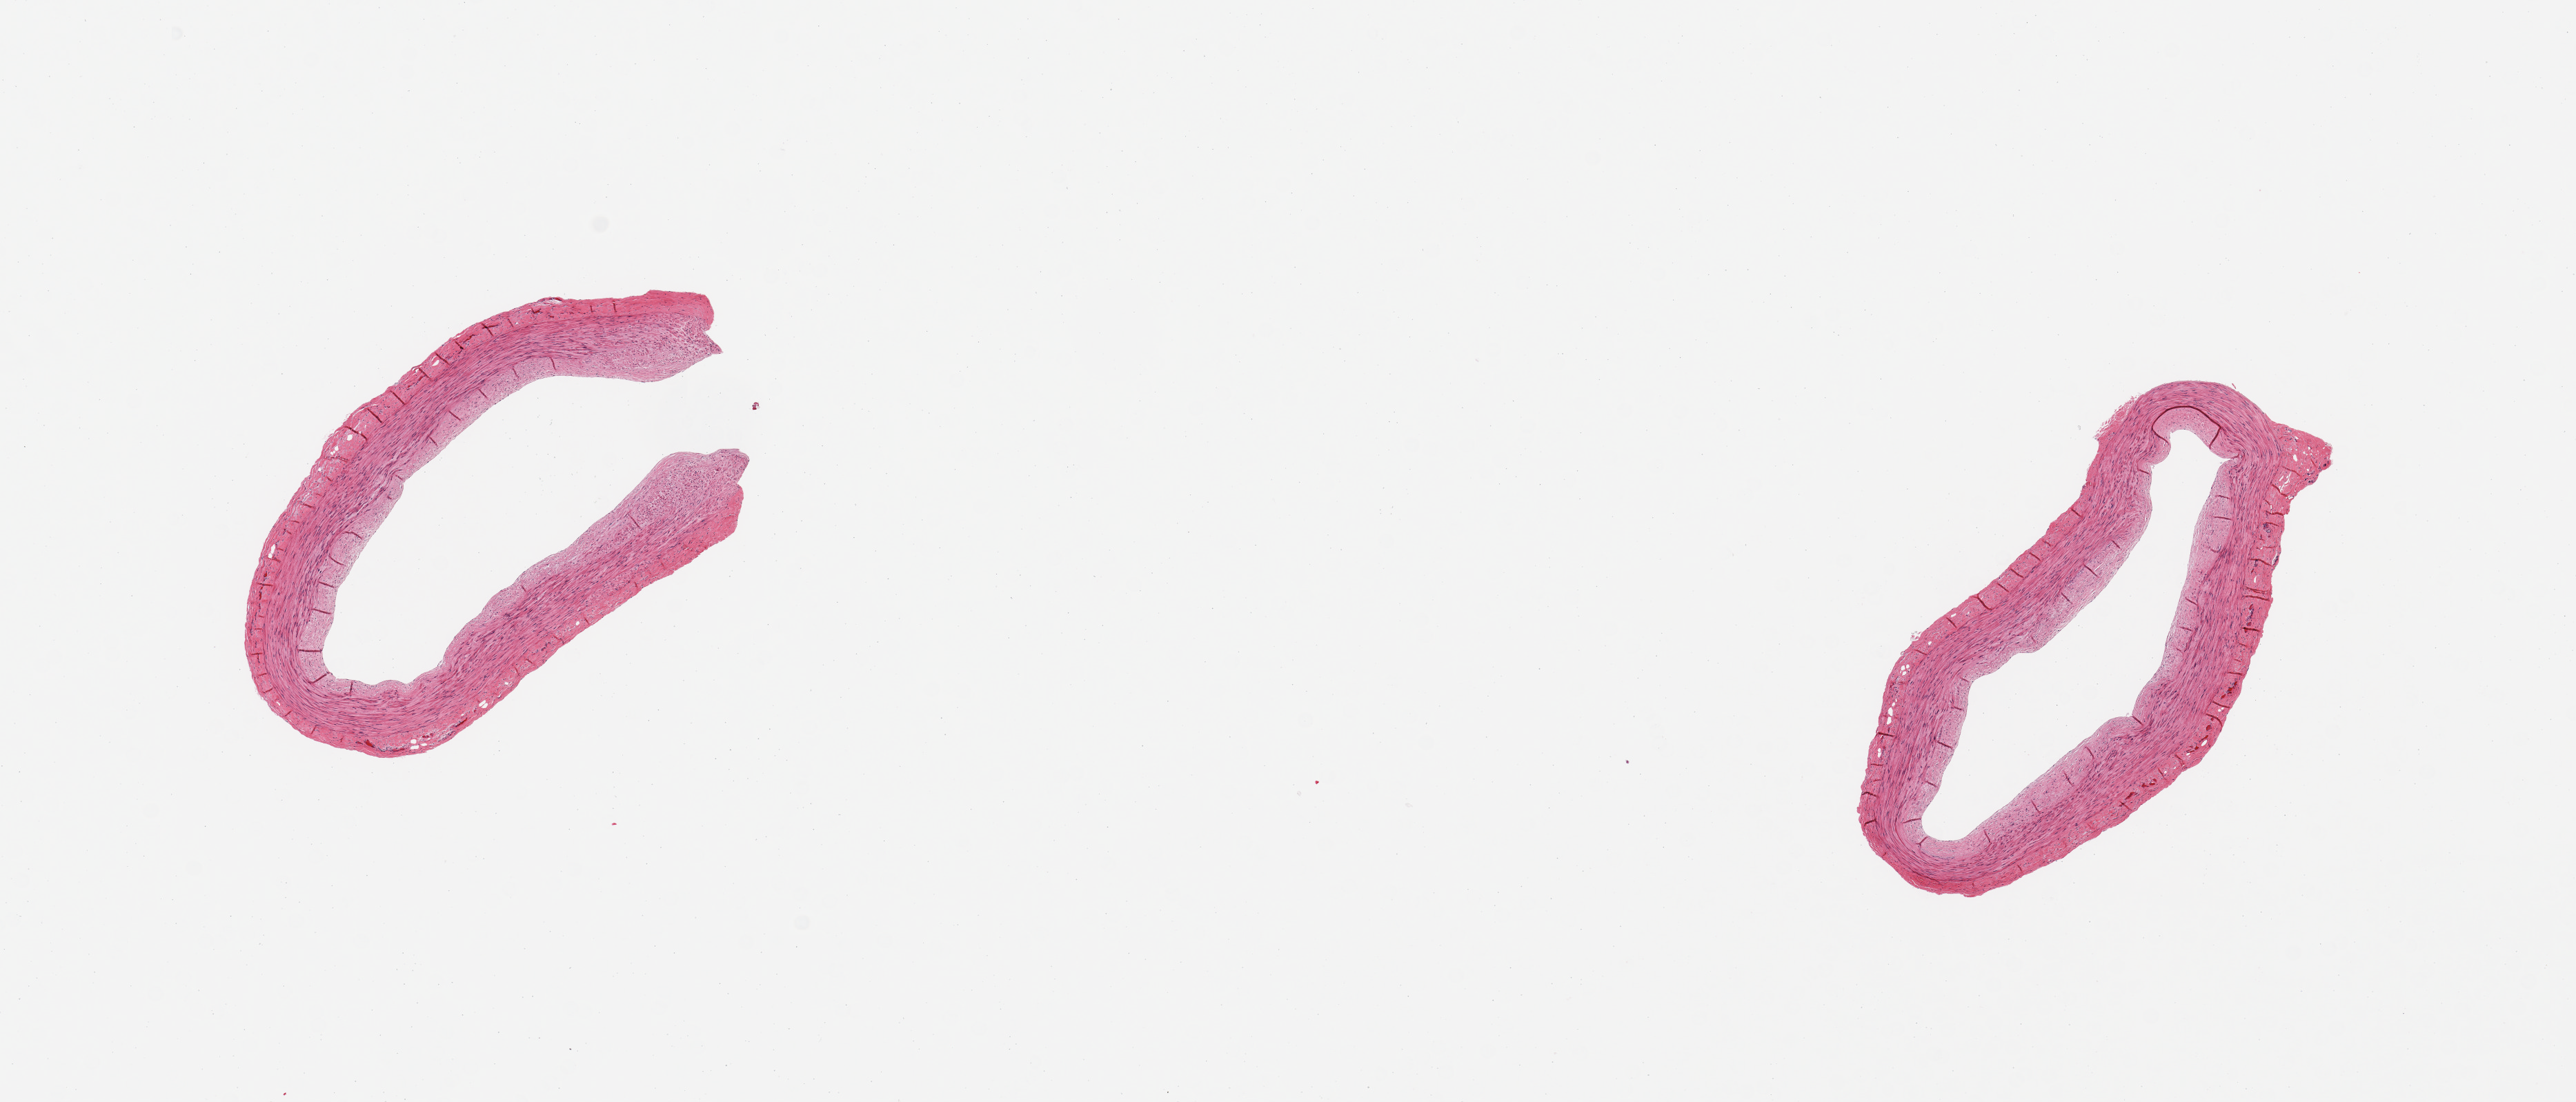
H&E whole-slide image, shown as a low-resolution overview of the whole scanned area (about 14.8 x 6.3 mm). PAXgene-fixed, paraffin-embedded tissue. Sampled site (target tissue): tibial artery. Donor tissue sample. Donor: male.
Review note (as recorded): 2 pieces, minimal atherosis, no adherent fat.